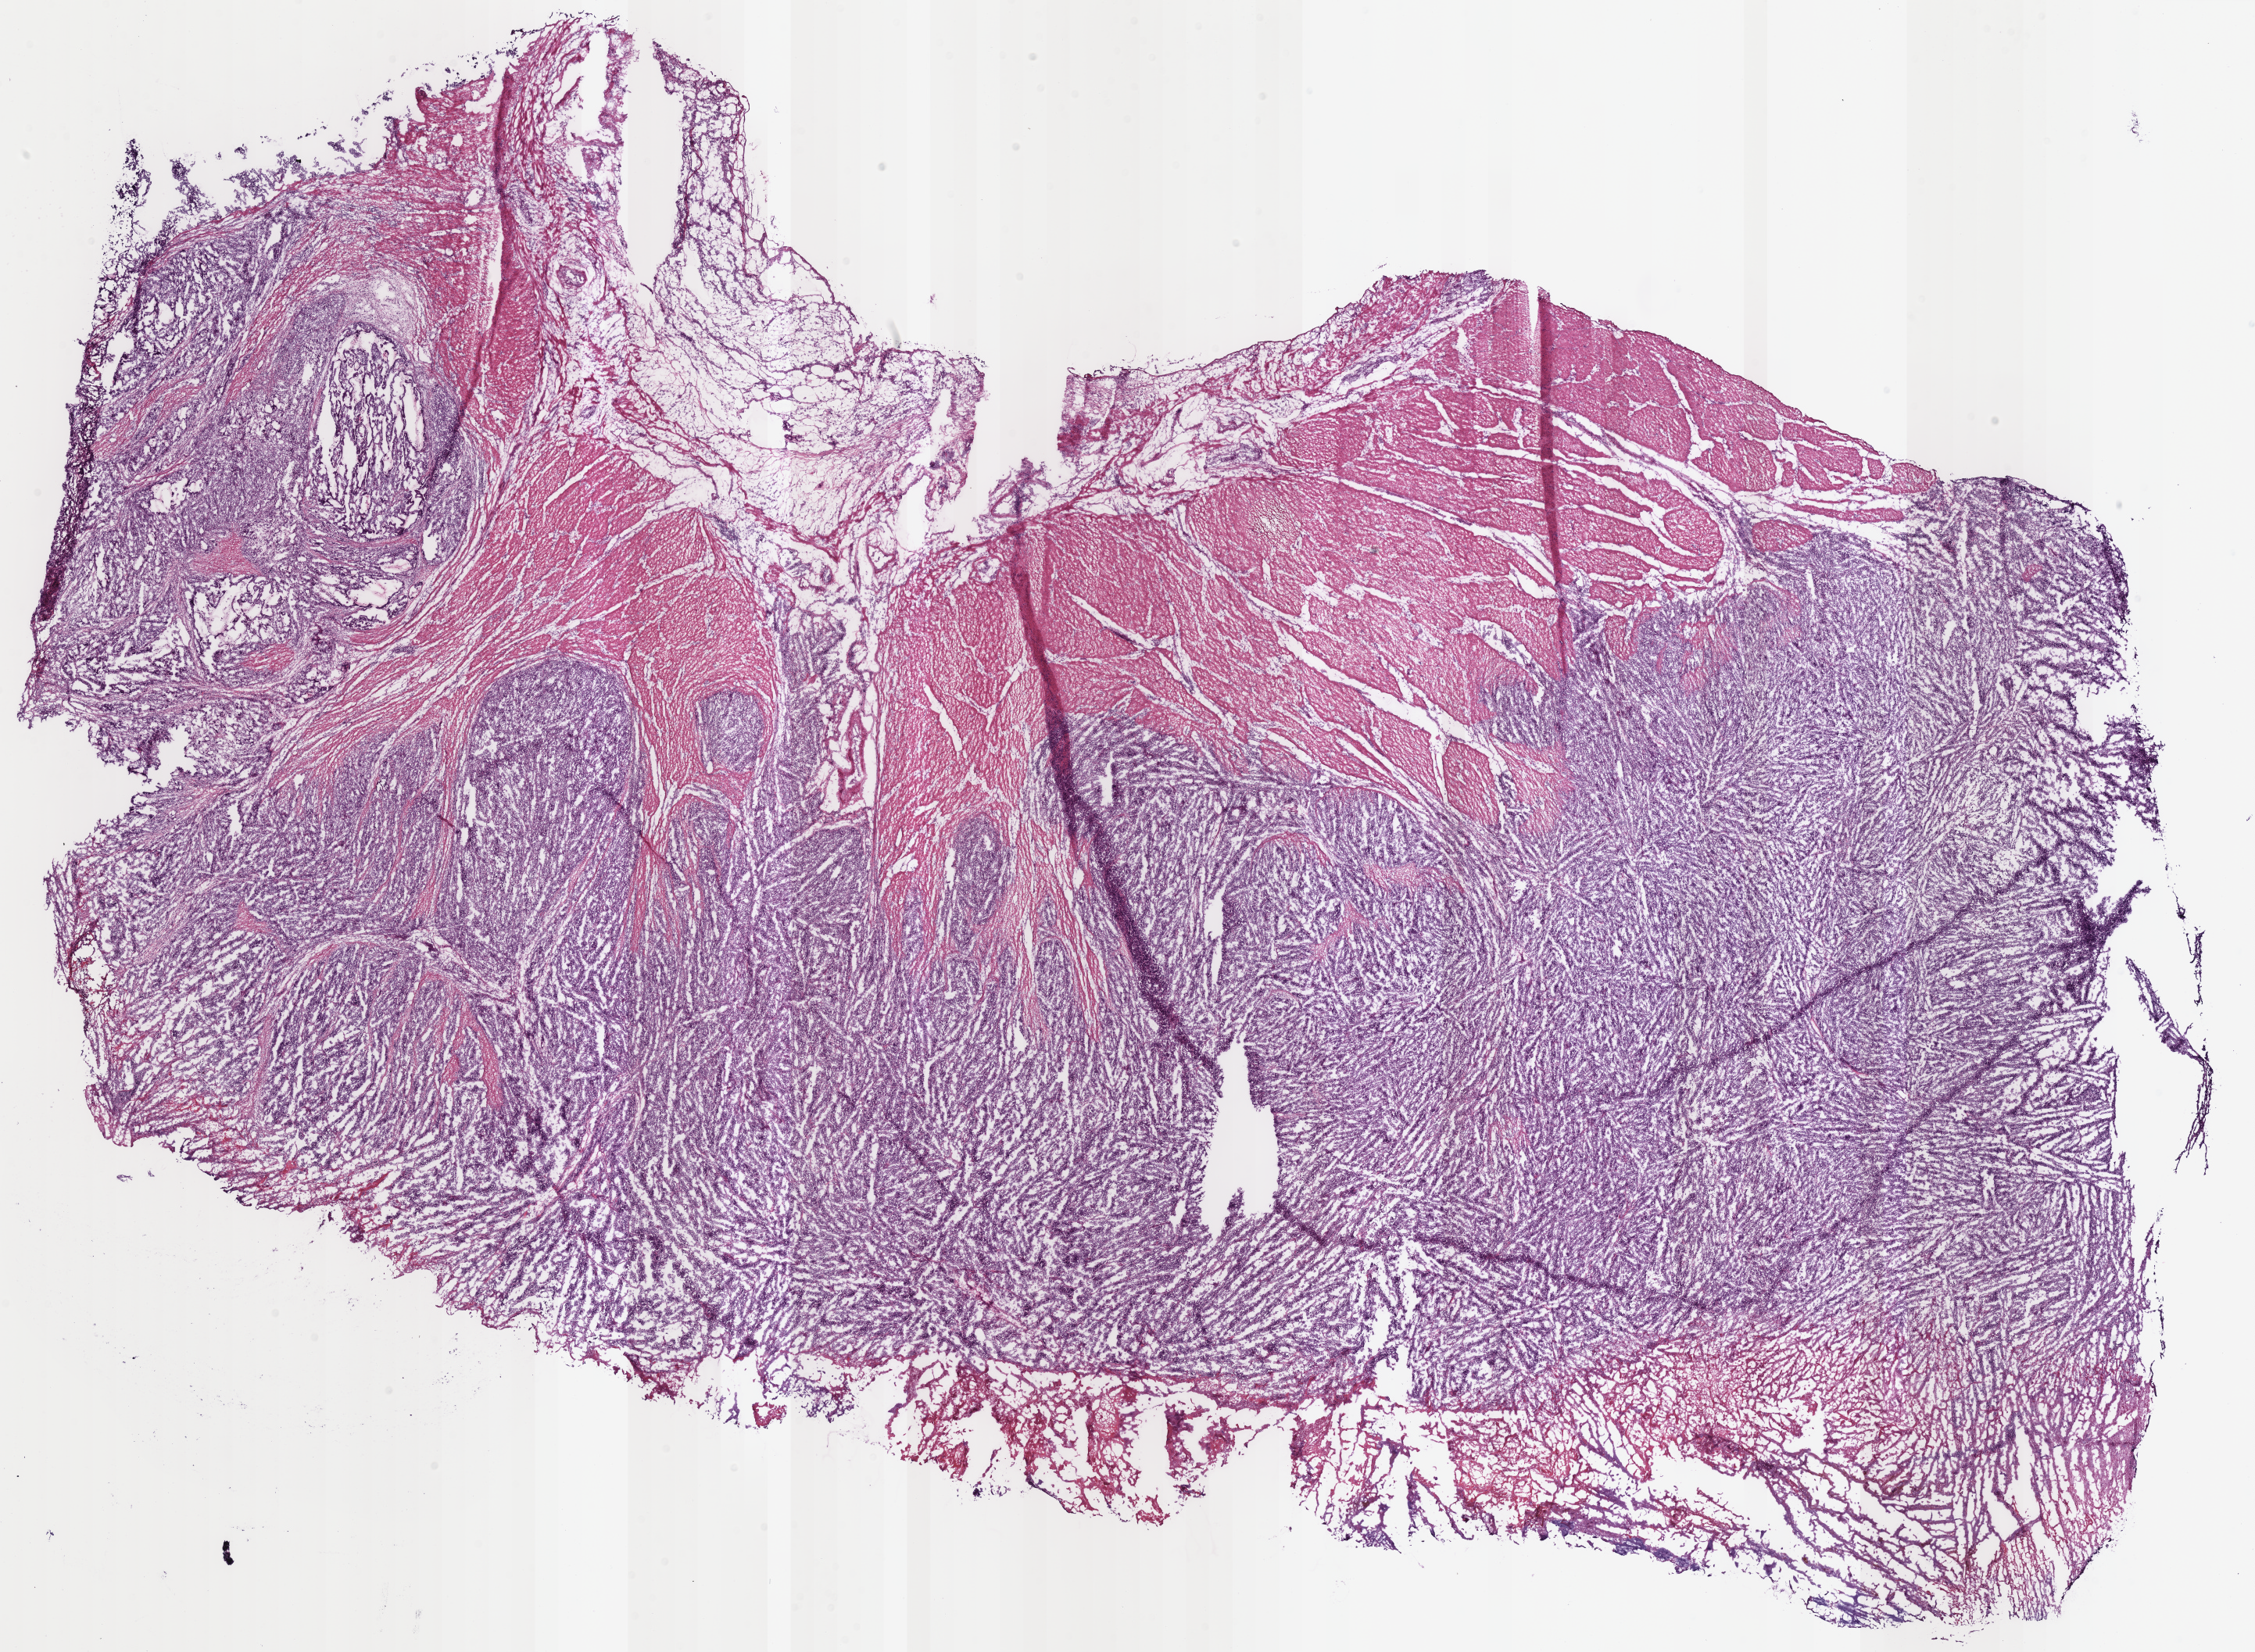
H&E whole-slide image — shown as a low-resolution overview of the whole scanned area (about 22.7 x 16.7 mm, acquisition: 40x scan), frozen section from the bottom of the tissue portion, primary tumour sample from the stomach. Male, age 59 years at initial diagnosis.
Pathologic diagnosis: Adenocarcinoma, intestinal type (gastric antrum).